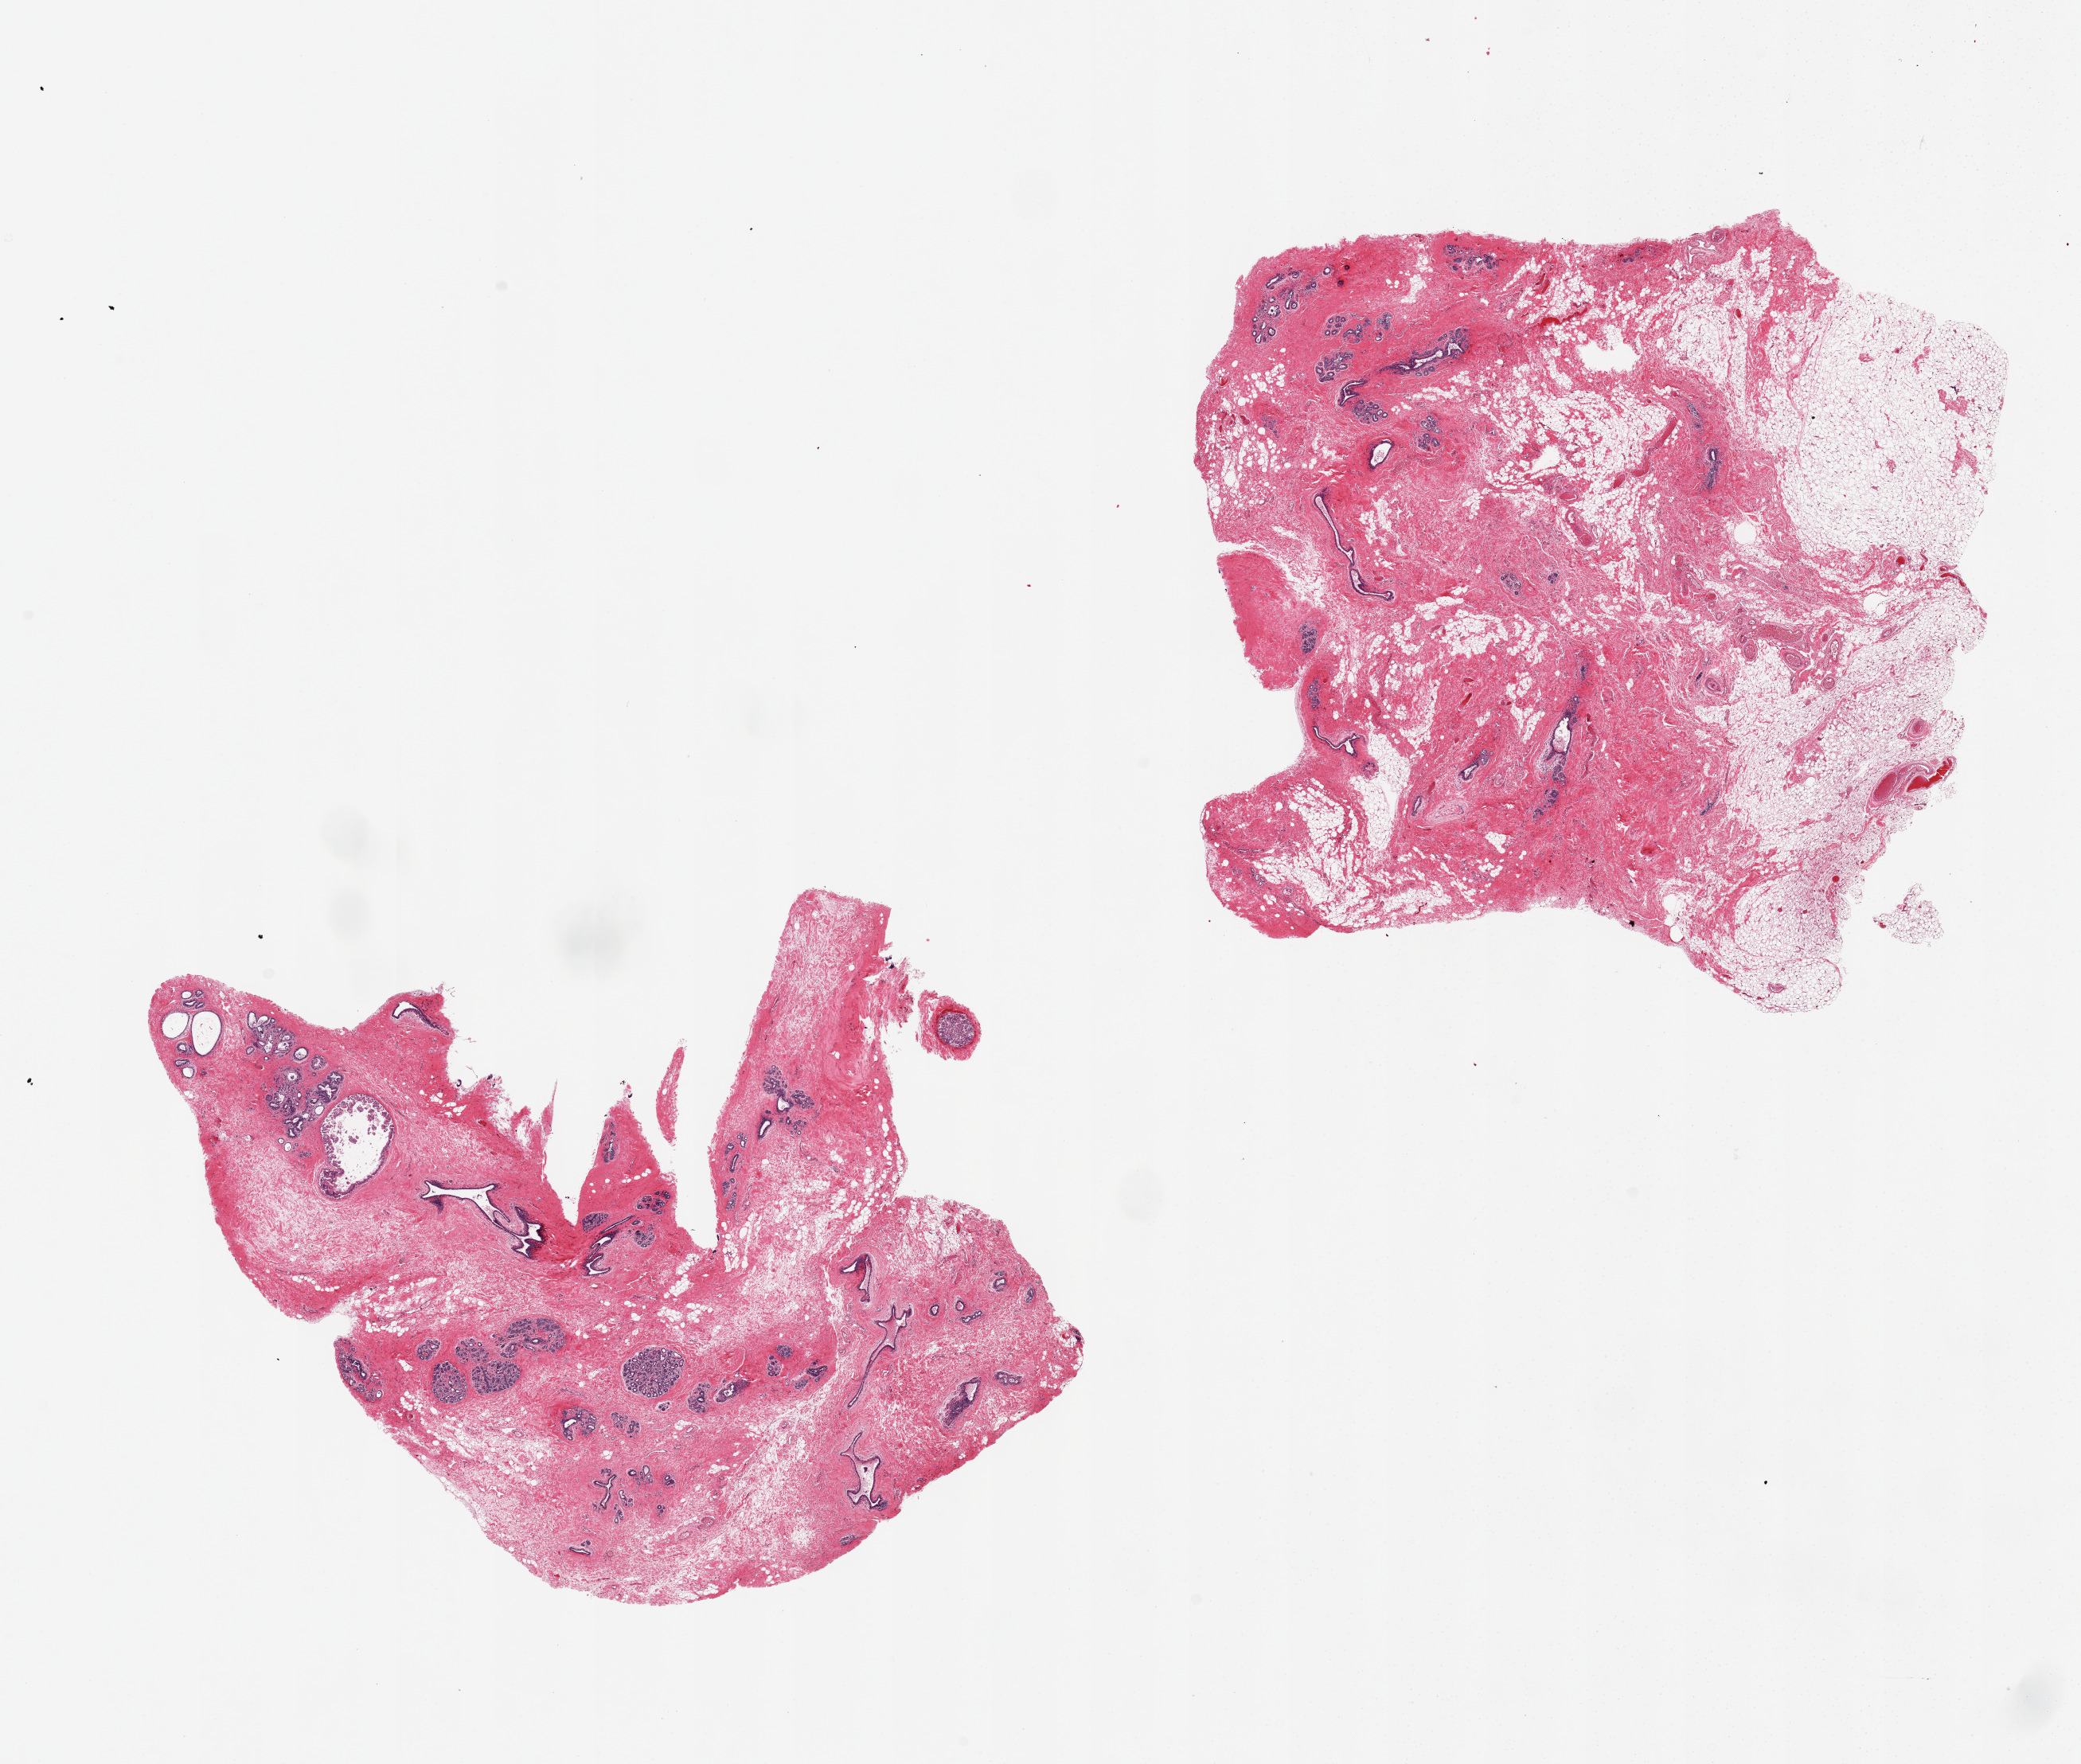
Haematoxylin and eosin whole-slide image, shown as a low-resolution overview of the whole scanned area (about 20.7 x 17.5 mm, slide scanned at 20x). PAXgene-fixed, paraffin-embedded tissue. Sampled site (target tissue): breast. Tissue donor sample. Donor sex: female.
Review note (as recorded): 2 pieces, TDLU's present, fibrocystic changd and duct ectasia; Some foci with modereate autolysis, approaching score 2.